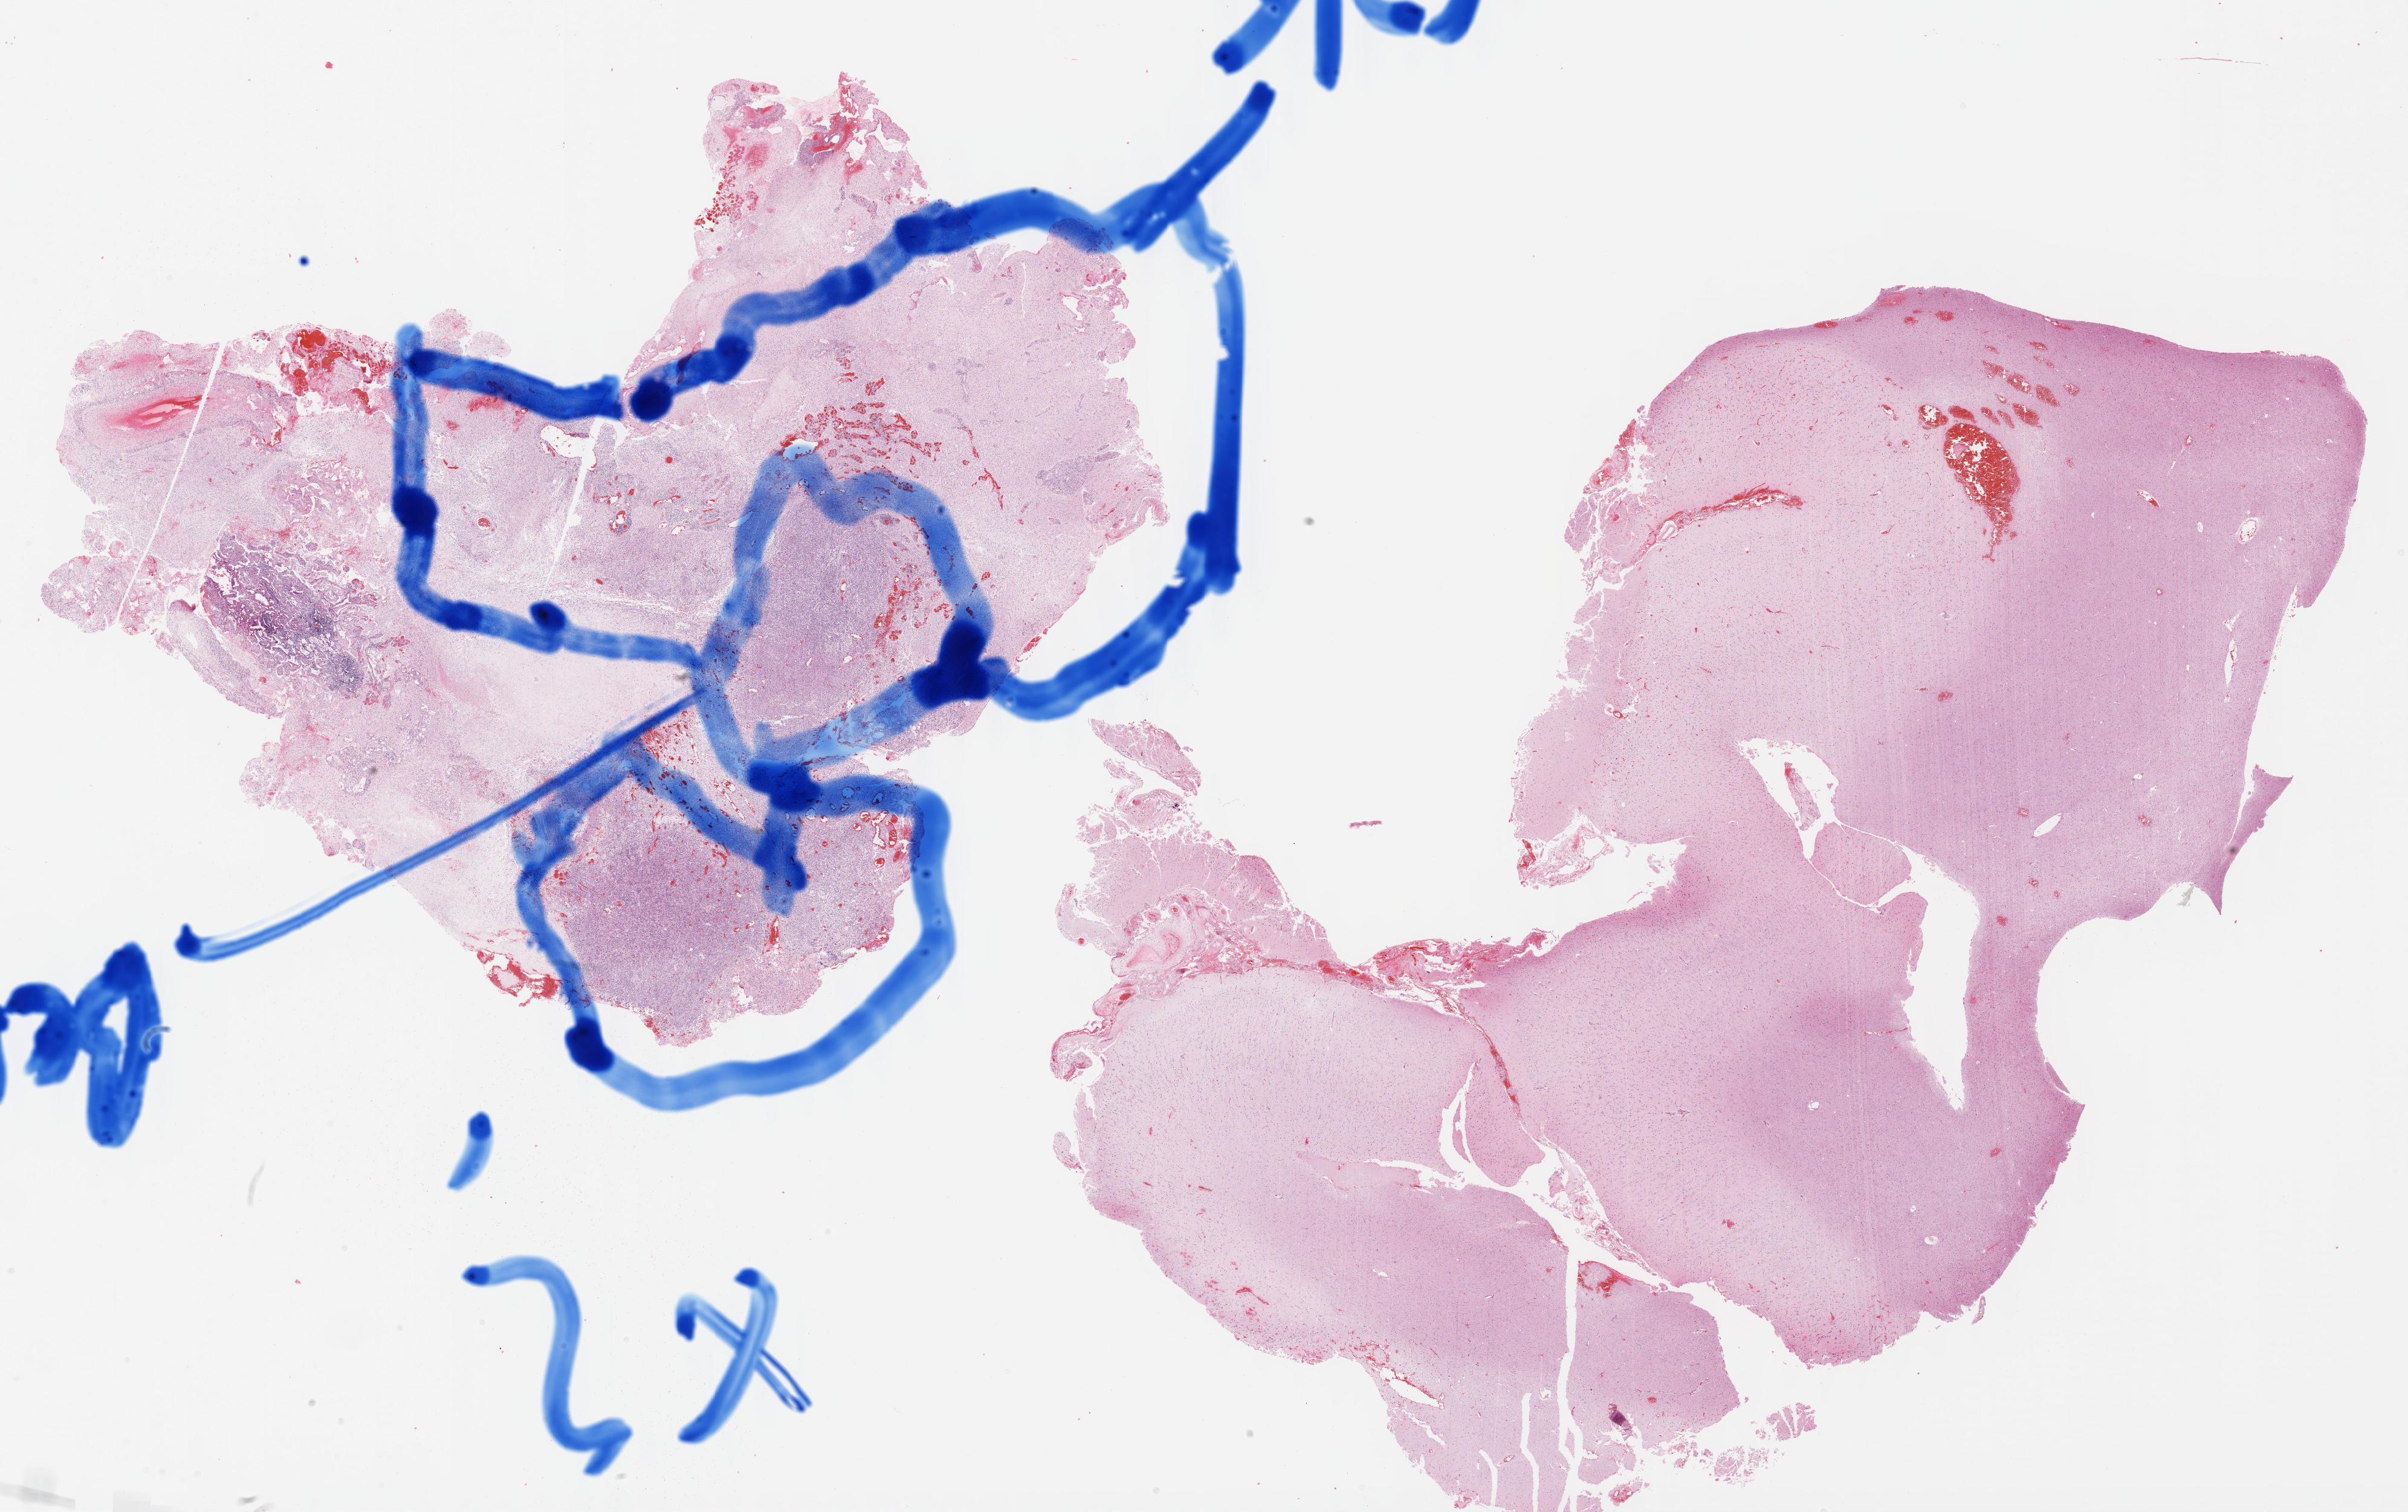
Whole-slide histology image, Hematoxylin and eosin (H&E) stained — shown as a low-resolution overview of the whole scanned area (about 32.2 x 20.2 mm, from a 40x scan); formalin-fixed paraffin-embedded (FFPE) diagnostic section; brain, primary tumour sample. Patient: male, age at initial diagnosis 60 years.
Diagnosis: Glioblastoma.